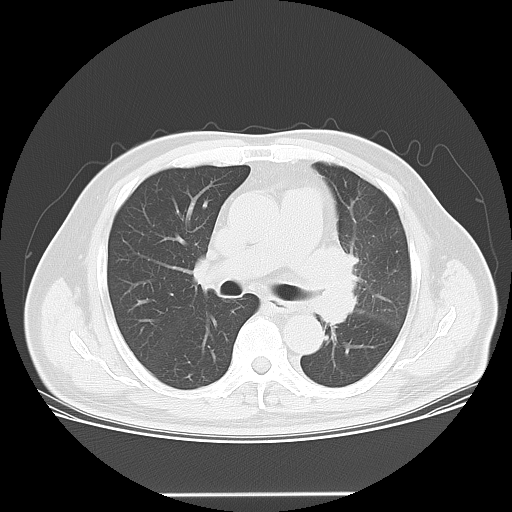
Chest CT, one axial slice; slice 34 of 55 in the series (ordered by position); reconstruction kernel LUNG; 120 kVp; lung window (W 1500 / L -600 HU); 5 mm slice thickness; 512 × 512 image matrix, field of view 398 × 398 mm. Male patient, age 61 years. From the clinical record (not read from this slice): clinical TNM (as recorded): T3 N1 M1; histopathological grade: G3.
Structures marked on this image (bounding box drawn by a radiologist):
- lung tumour (recorded histology: small cell carcinoma): bounding box [x1, y1, x2, y2] px = [317, 242, 369, 334]